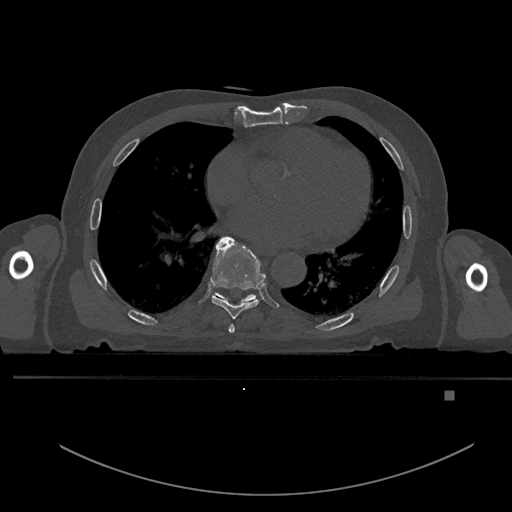
CT including the spine, one axial slice. Slice 242 of 969 in the series (ordered by position). Bone window (W 1800 / L 400 HU). 0.5 mm slice thickness. 512 × 512 image matrix, field of view 456 × 456 mm. Patient: male, 82 years. From the clinical record (not read from this slice): primary cancer: prostate; vertebrae with lytic lesions (as recorded): T11, T9, T8, T2.
Structures marked on this image (semi-automatically segmented with operator editing):
- T6 vertebra: bounding box [x1, y1, x2, y2] px = [229, 324, 235, 333]
- T7 vertebra: [211, 236, 266, 319]
- T8 vertebra: [211, 292, 257, 304]